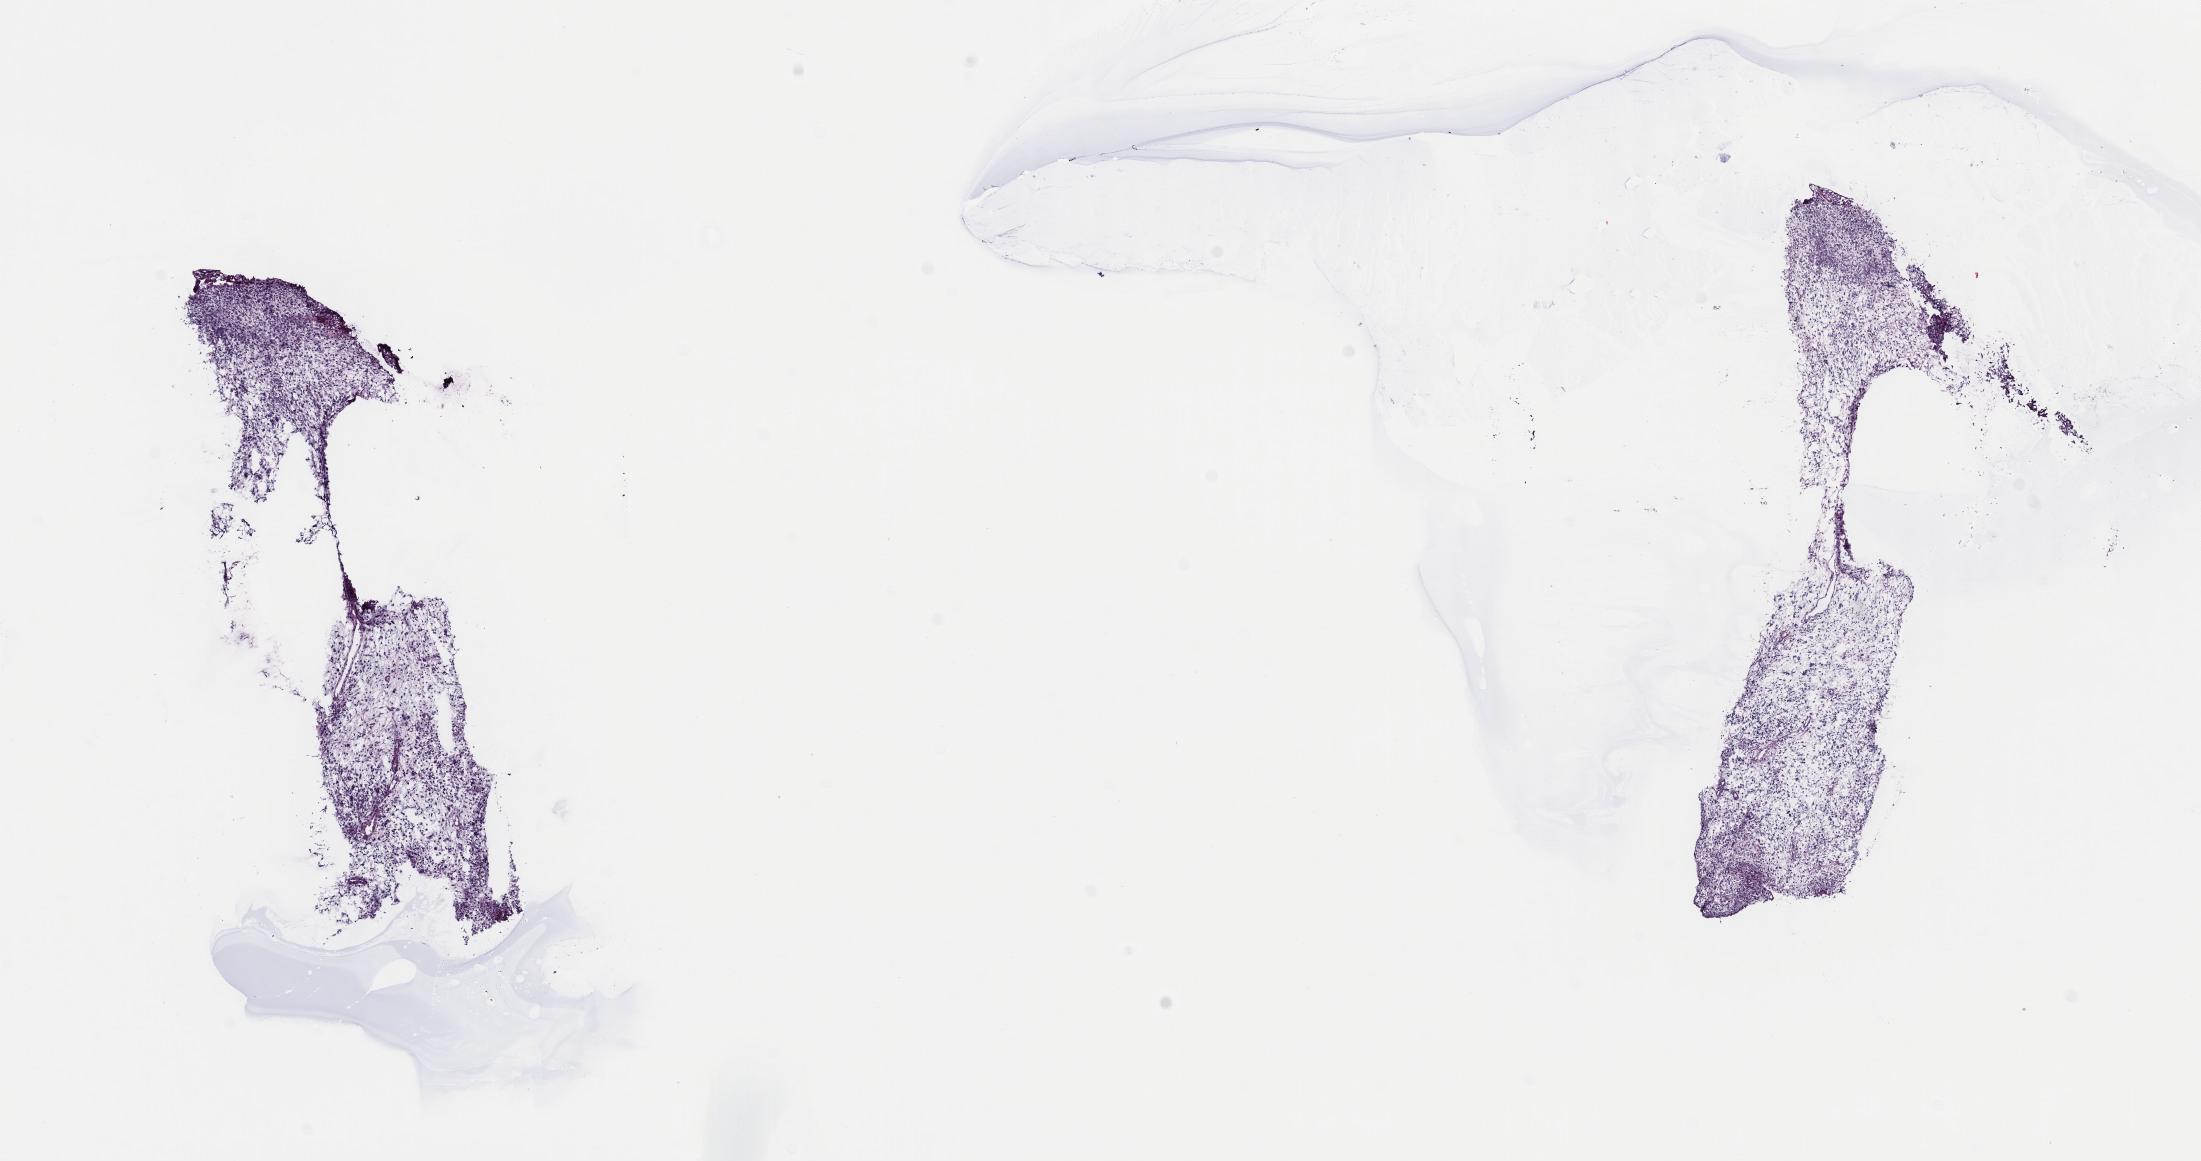
Whole-slide histology image, H&E — whole scanned area (about 17.4 x 9.2 mm, acquisition: 40x scan) shown as a low-resolution overview; frozen section from the top of the tissue portion; primary tumour sample from the uterus. Female patient; age at initial diagnosis 76 years. Pathologist review of this section (percent, as recorded): tumour cells 90%, tumour nuclei 90%, normal cells 0%, stromal cells 5%, necrosis 5%. Inflammatory infiltration, as recorded: lymphocyte infiltration 40%, monocyte infiltration 20%, neutrophil infiltration 20%.
FIGO stage: IIIC2. Pathologic diagnosis: Mullerian mixed tumor (endometrium).